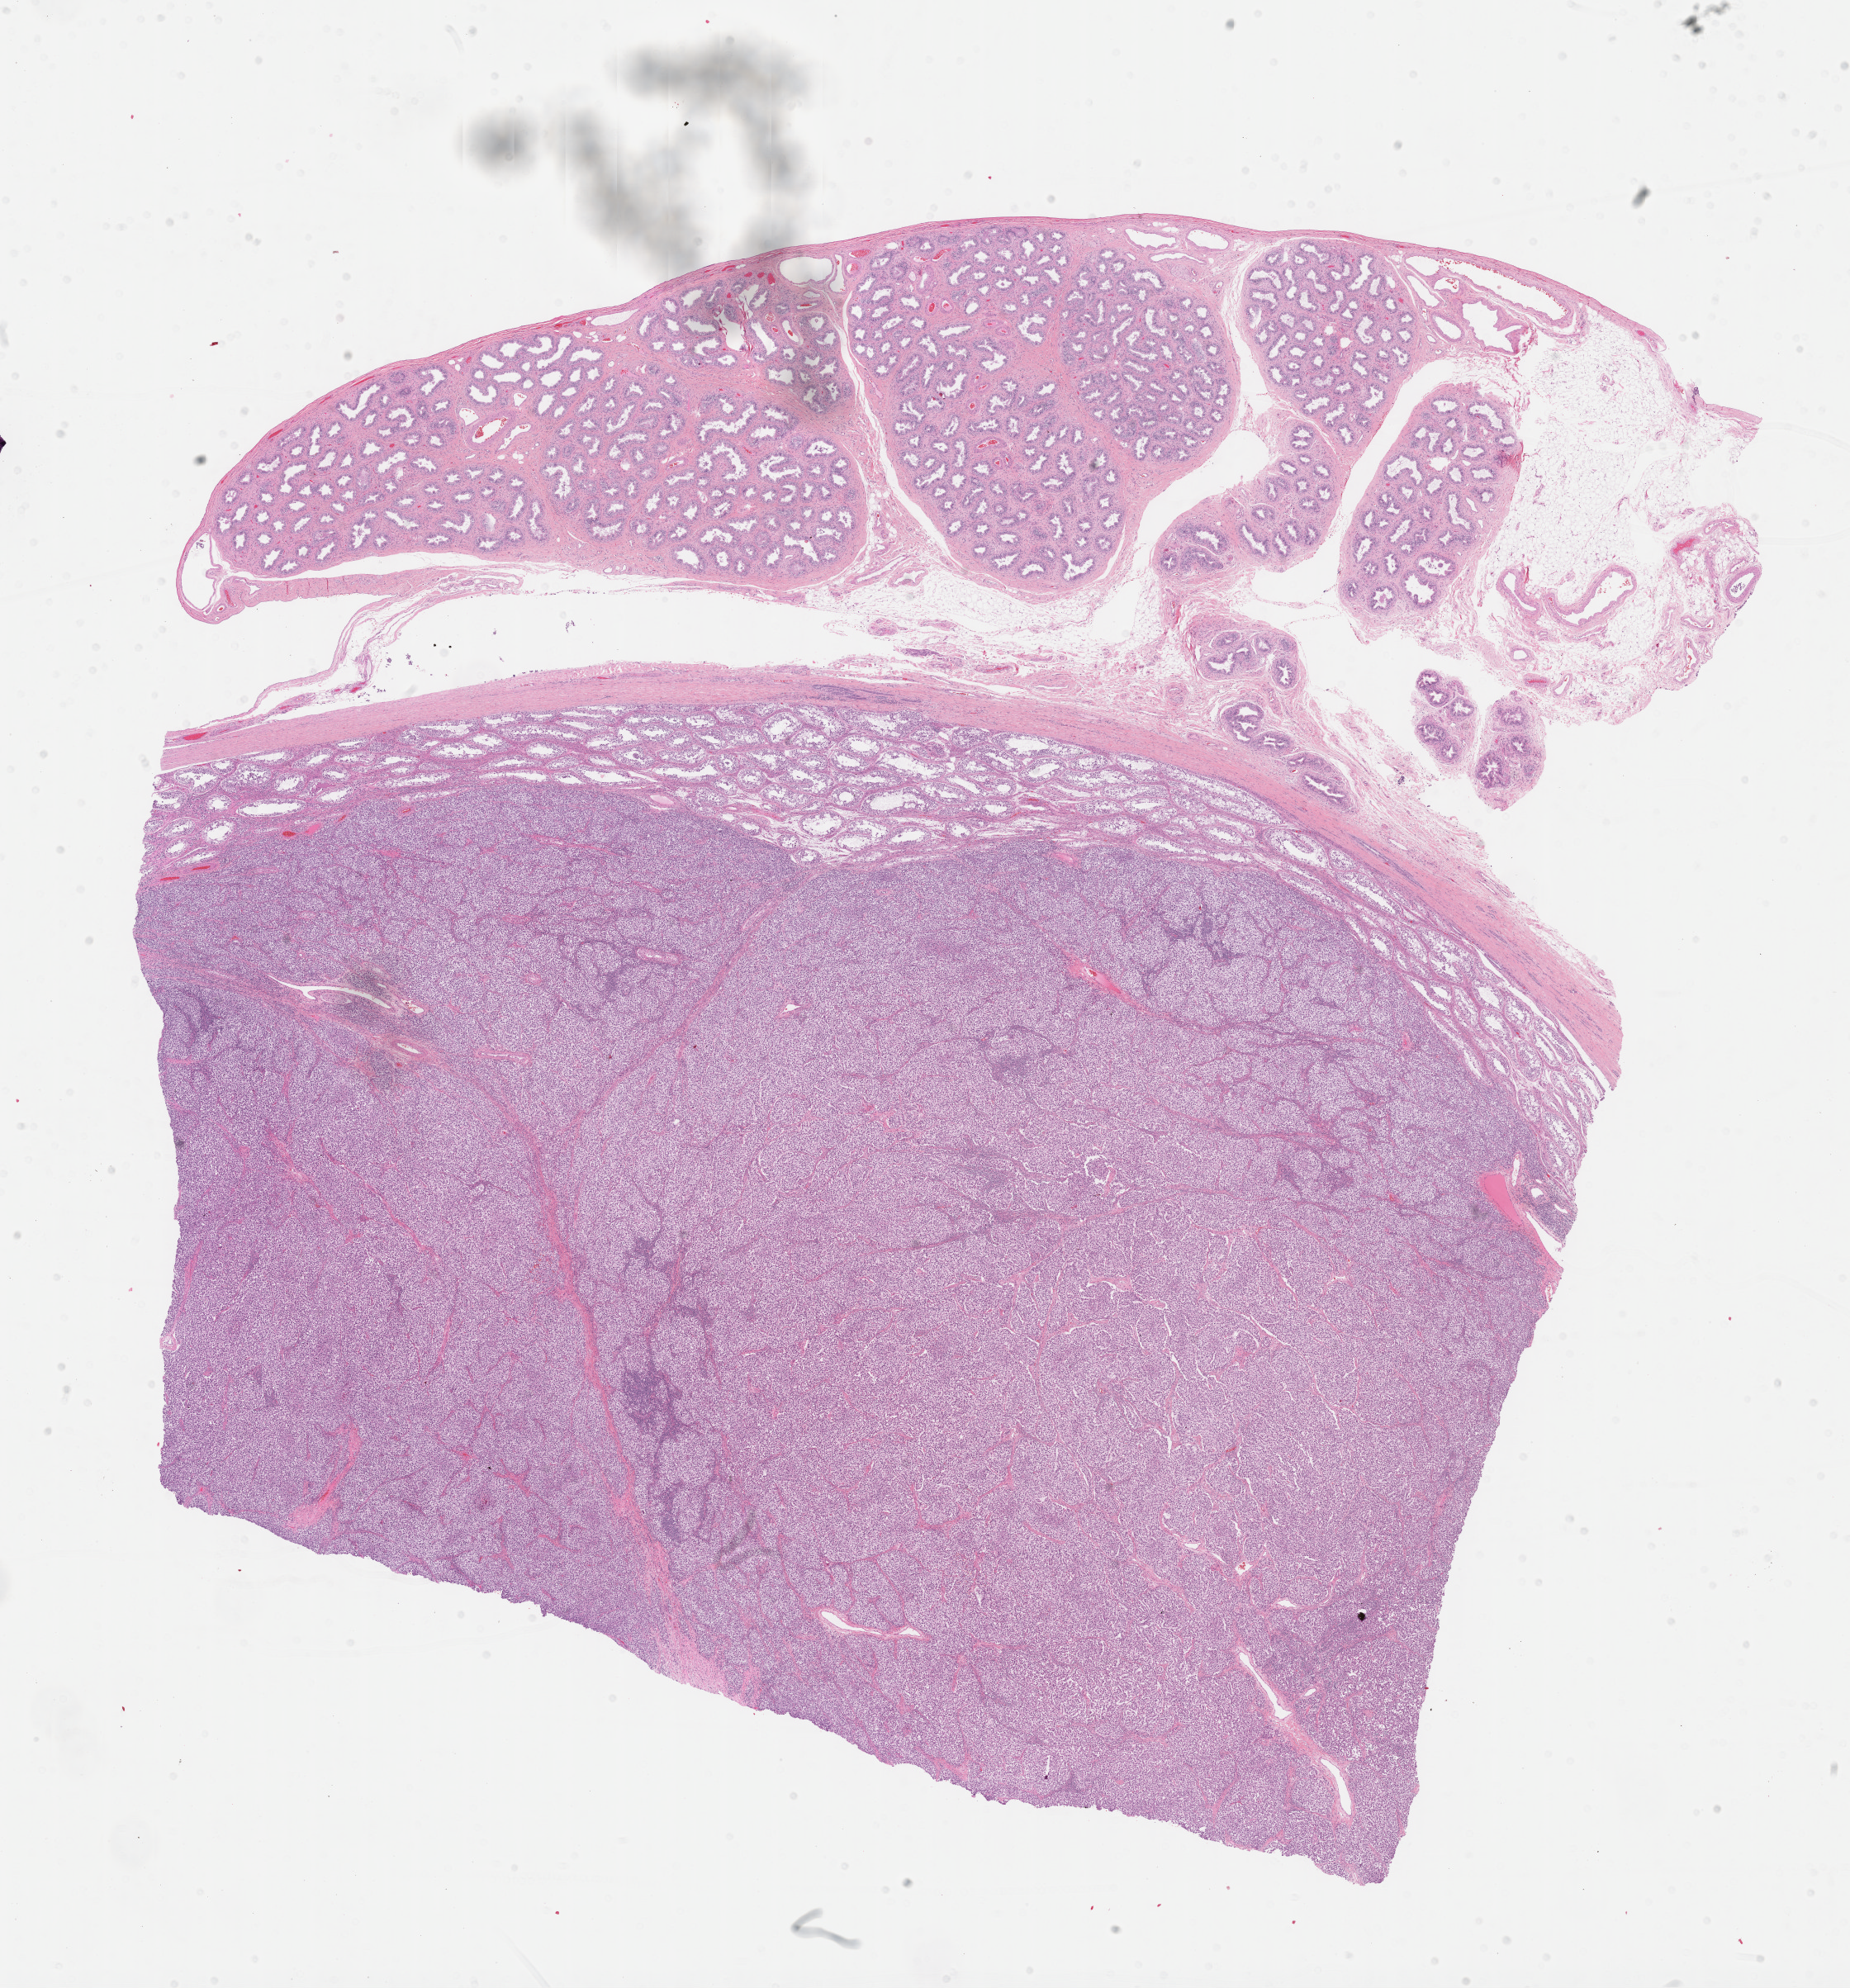
Whole-slide histology image, Hematoxylin and eosin (H&E) stained — low-resolution overview of the scanned area, about 18.1 x 19.5 mm (from a 40x scan), formalin-fixed paraffin-embedded (FFPE) diagnostic section, primary tumour sample from the testis. Patient: male, age at initial diagnosis 38 years.
- pathologic diagnosis: Seminoma, NOS
- laterality: left